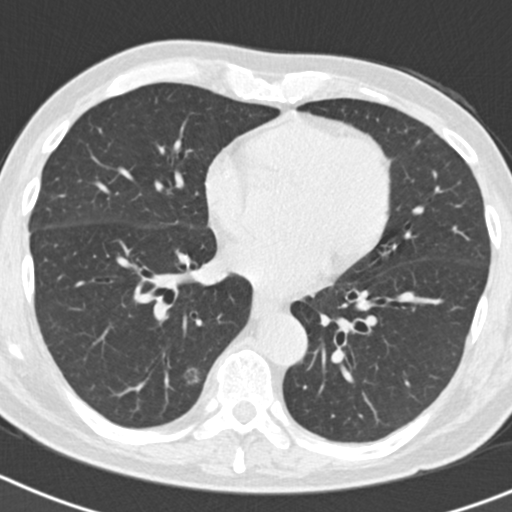
Low-dose screening chest CT, axial slice; second screening round (one year after baseline); lung window (W 1500 / L -600 HU); 120 kVp; 512 × 512 image matrix, field of view 300 × 300 mm. Male participant, aged 70 years at enrolment. Current smoker at enrolment.
Lesion marked by an expert reader, box from (x=123, y=355) to (x=210, y=430) px. The screening reader recorded 5 non-calcified nodules or masses ≥4 mm on this exam (right lower lobe, right lower lobe, right upper lobe, right upper lobe, left upper lobe); which of them this box marks is not recorded. Participant outcome: lung cancer diagnosed 622 days after this screen — bronchiolo-alveolar adenocarcinoma, NOS, right lower lobe, poorly differentiated (G3), stage IB (AJCC 6th edition), 30 mm at pathology.